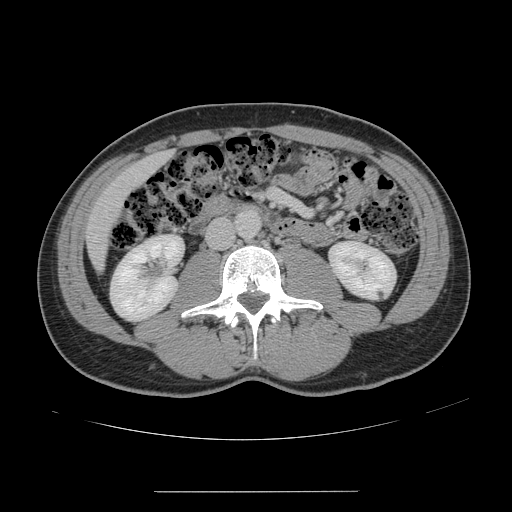
Contrast-enhanced abdominal CT, one axial slice. Position 38 of 178 along the scan axis. Intravenous contrast given. Soft-tissue window (W 400 / L 40 HU). 2.5 mm slice thickness. 512 × 512 image matrix. Male patient, age 53 years. From the clinical record (not read from this slice): diagnosis: colorectal cancer liver metastases, imaged before liver resection; multiple liver metastases: yes; largest metastasis: 2.4 cm.
Outlined on this slice (expert manual segmentation):
- liver: bounding box (x1, y1, x2, y2) in pixels: (88, 153, 169, 268)